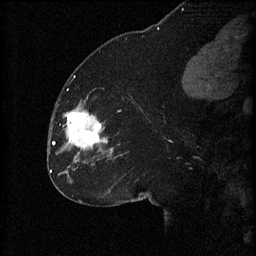
Breast MRI (dynamic contrast-enhanced), one sagittal slice; position 28 of 60 along the scan axis; 3 images stored at this slice position (order not interpretable as contrast timing); 1.5 T; TE 4.2 ms, TR 8.2 ms; 2 mm slice thickness; 256 × 256 image matrix, field of view 180 × 180 mm. Female patient, age 32 years.
Annotated regions visible in this slice (semi-automatically segmented with operator editing):
- analysis volume of interest (the breast-tissue region the enhancement analysis was run in; not a lesion): bounding box <58,106,111,165> (left, top, right, bottom; pixels)
- tumour enhancement mask (voxels above the 70 % enhancement threshold inside the analysis volume of interest): <64,108,107,149>